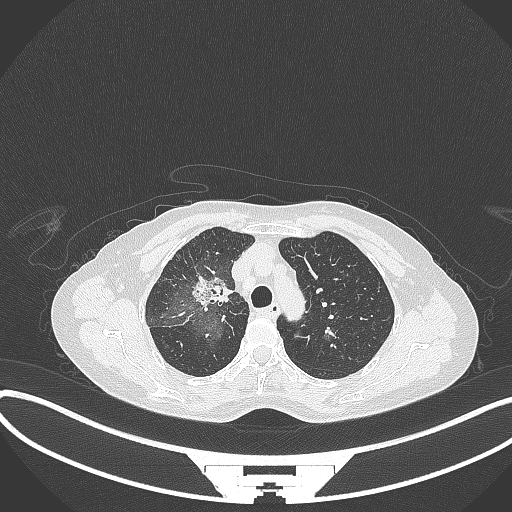
Chest CT, one axial slice; reconstruction kernel B70f; lung window (W 1500 / L -600 HU); 512 × 512 image matrix. Patient: female, 59 years. Case-level facts recorded for this patient, not image findings: clinical TNM (as recorded): T3 N0 M0; histopathological grade: G1.
Outlined on this slice (bounding box drawn by a radiologist):
- lung tumour (recorded histology: adenocarcinoma): bounding box (x1, y1, x2, y2) in pixels: (193, 267, 233, 312)